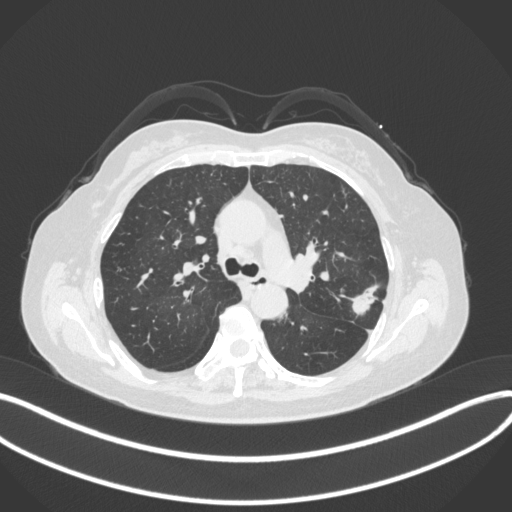
Chest CT, one axial slice; slice 221 of 330 in the series (ordered by position); reconstruction kernel B31f; lung window (W 1500 / L -600 HU); 1 mm slice thickness; 512 × 512 image matrix. Patient: female, 60 years. Case-level facts recorded for this patient, not image findings: clinical TNM (as recorded): T1c N0 M0.
Structures marked on this image (bounding box drawn by a radiologist):
- lung tumour (recorded histology: adenocarcinoma): bounding box <348,275,380,318> (left, top, right, bottom; pixels)